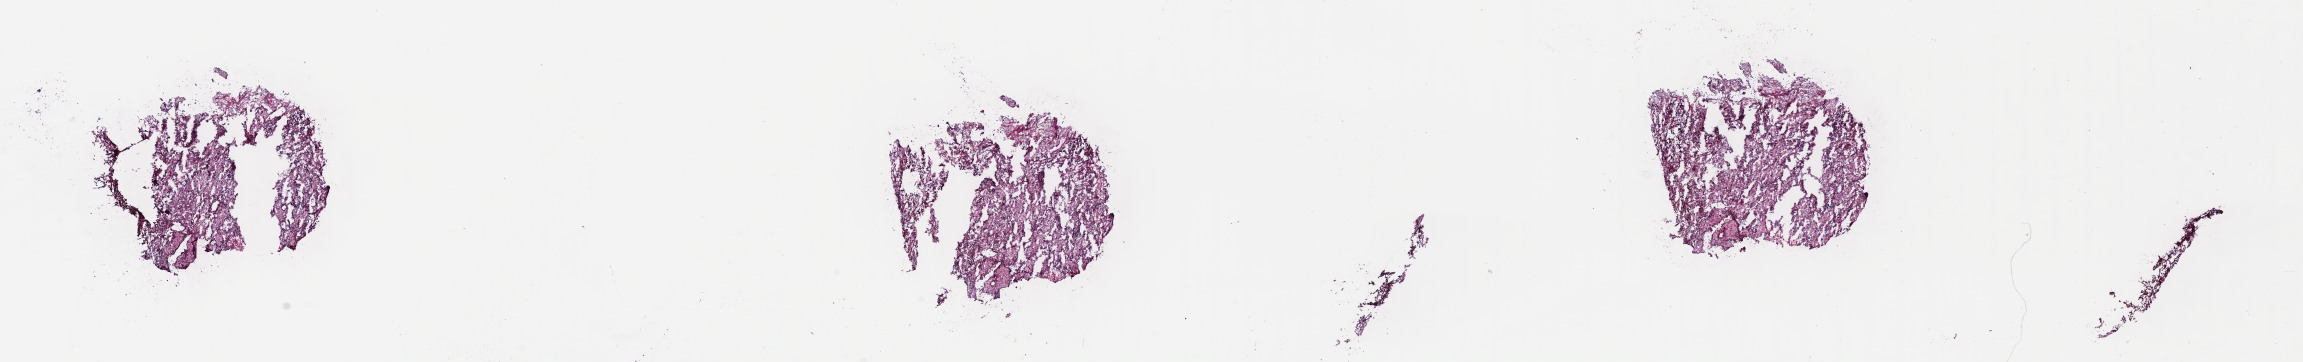
Whole-slide histology image, H&E-stained — shown as a low-resolution overview of the whole scanned area (about 37.2 x 5.9 mm), frozen section from the top of the tissue portion, primary tumour sample from the kidney. Male, age 80 years at initial diagnosis. Pathologist review of this section (percent, as recorded): tumour cells 100%, tumour nuclei 75%, normal cells 0%, stromal cells 0%, necrosis 0%. Inflammatory infiltration, as recorded: lymphocyte infiltration 1%, monocyte infiltration 5%, neutrophil infiltration 0%.
Laterality: left. Histologic diagnosis: Papillary adenocarcinoma, NOS.